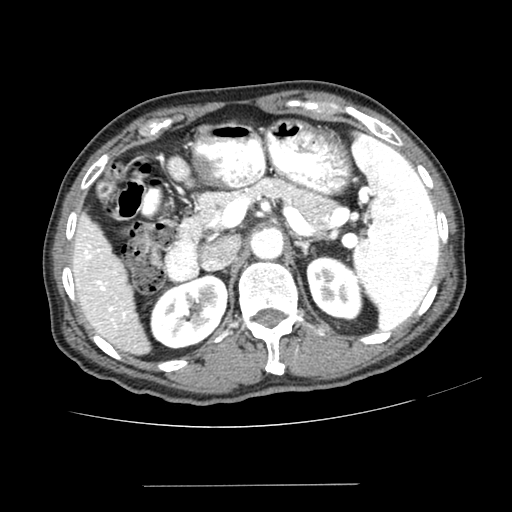
Contrast-enhanced abdominal CT (liver protocol), one axial slice; slice 145 of 187 in the series (ordered by position); reconstruction kernel SOFT; one of 2 acquisitions stored at this slice position; soft-tissue window (W 400 / L 40 HU); 2.5 mm slice thickness; 512 × 512 image matrix, field of view 360 × 360 mm. Case-level facts recorded for this patient, not image findings: diagnosis: hepatocellular carcinoma (patient treated with transarterial chemoembolisation; whether this scan precedes or follows treatment is not stated here); TNM stage (as recorded): Stage-I; Child-Pugh class: A; tumour differentiation: poorly differentiated; tumour size: 1.6 cm.
Annotated regions visible in this slice (semi-automatically segmented with operator editing):
- liver parenchyma outside the tumour (the mass and vessels are separate outlines, so this box may not span the whole liver): bounding box <72,212,150,354> (left, top, right, bottom; pixels)
- liver vessels: <75,229,128,328>